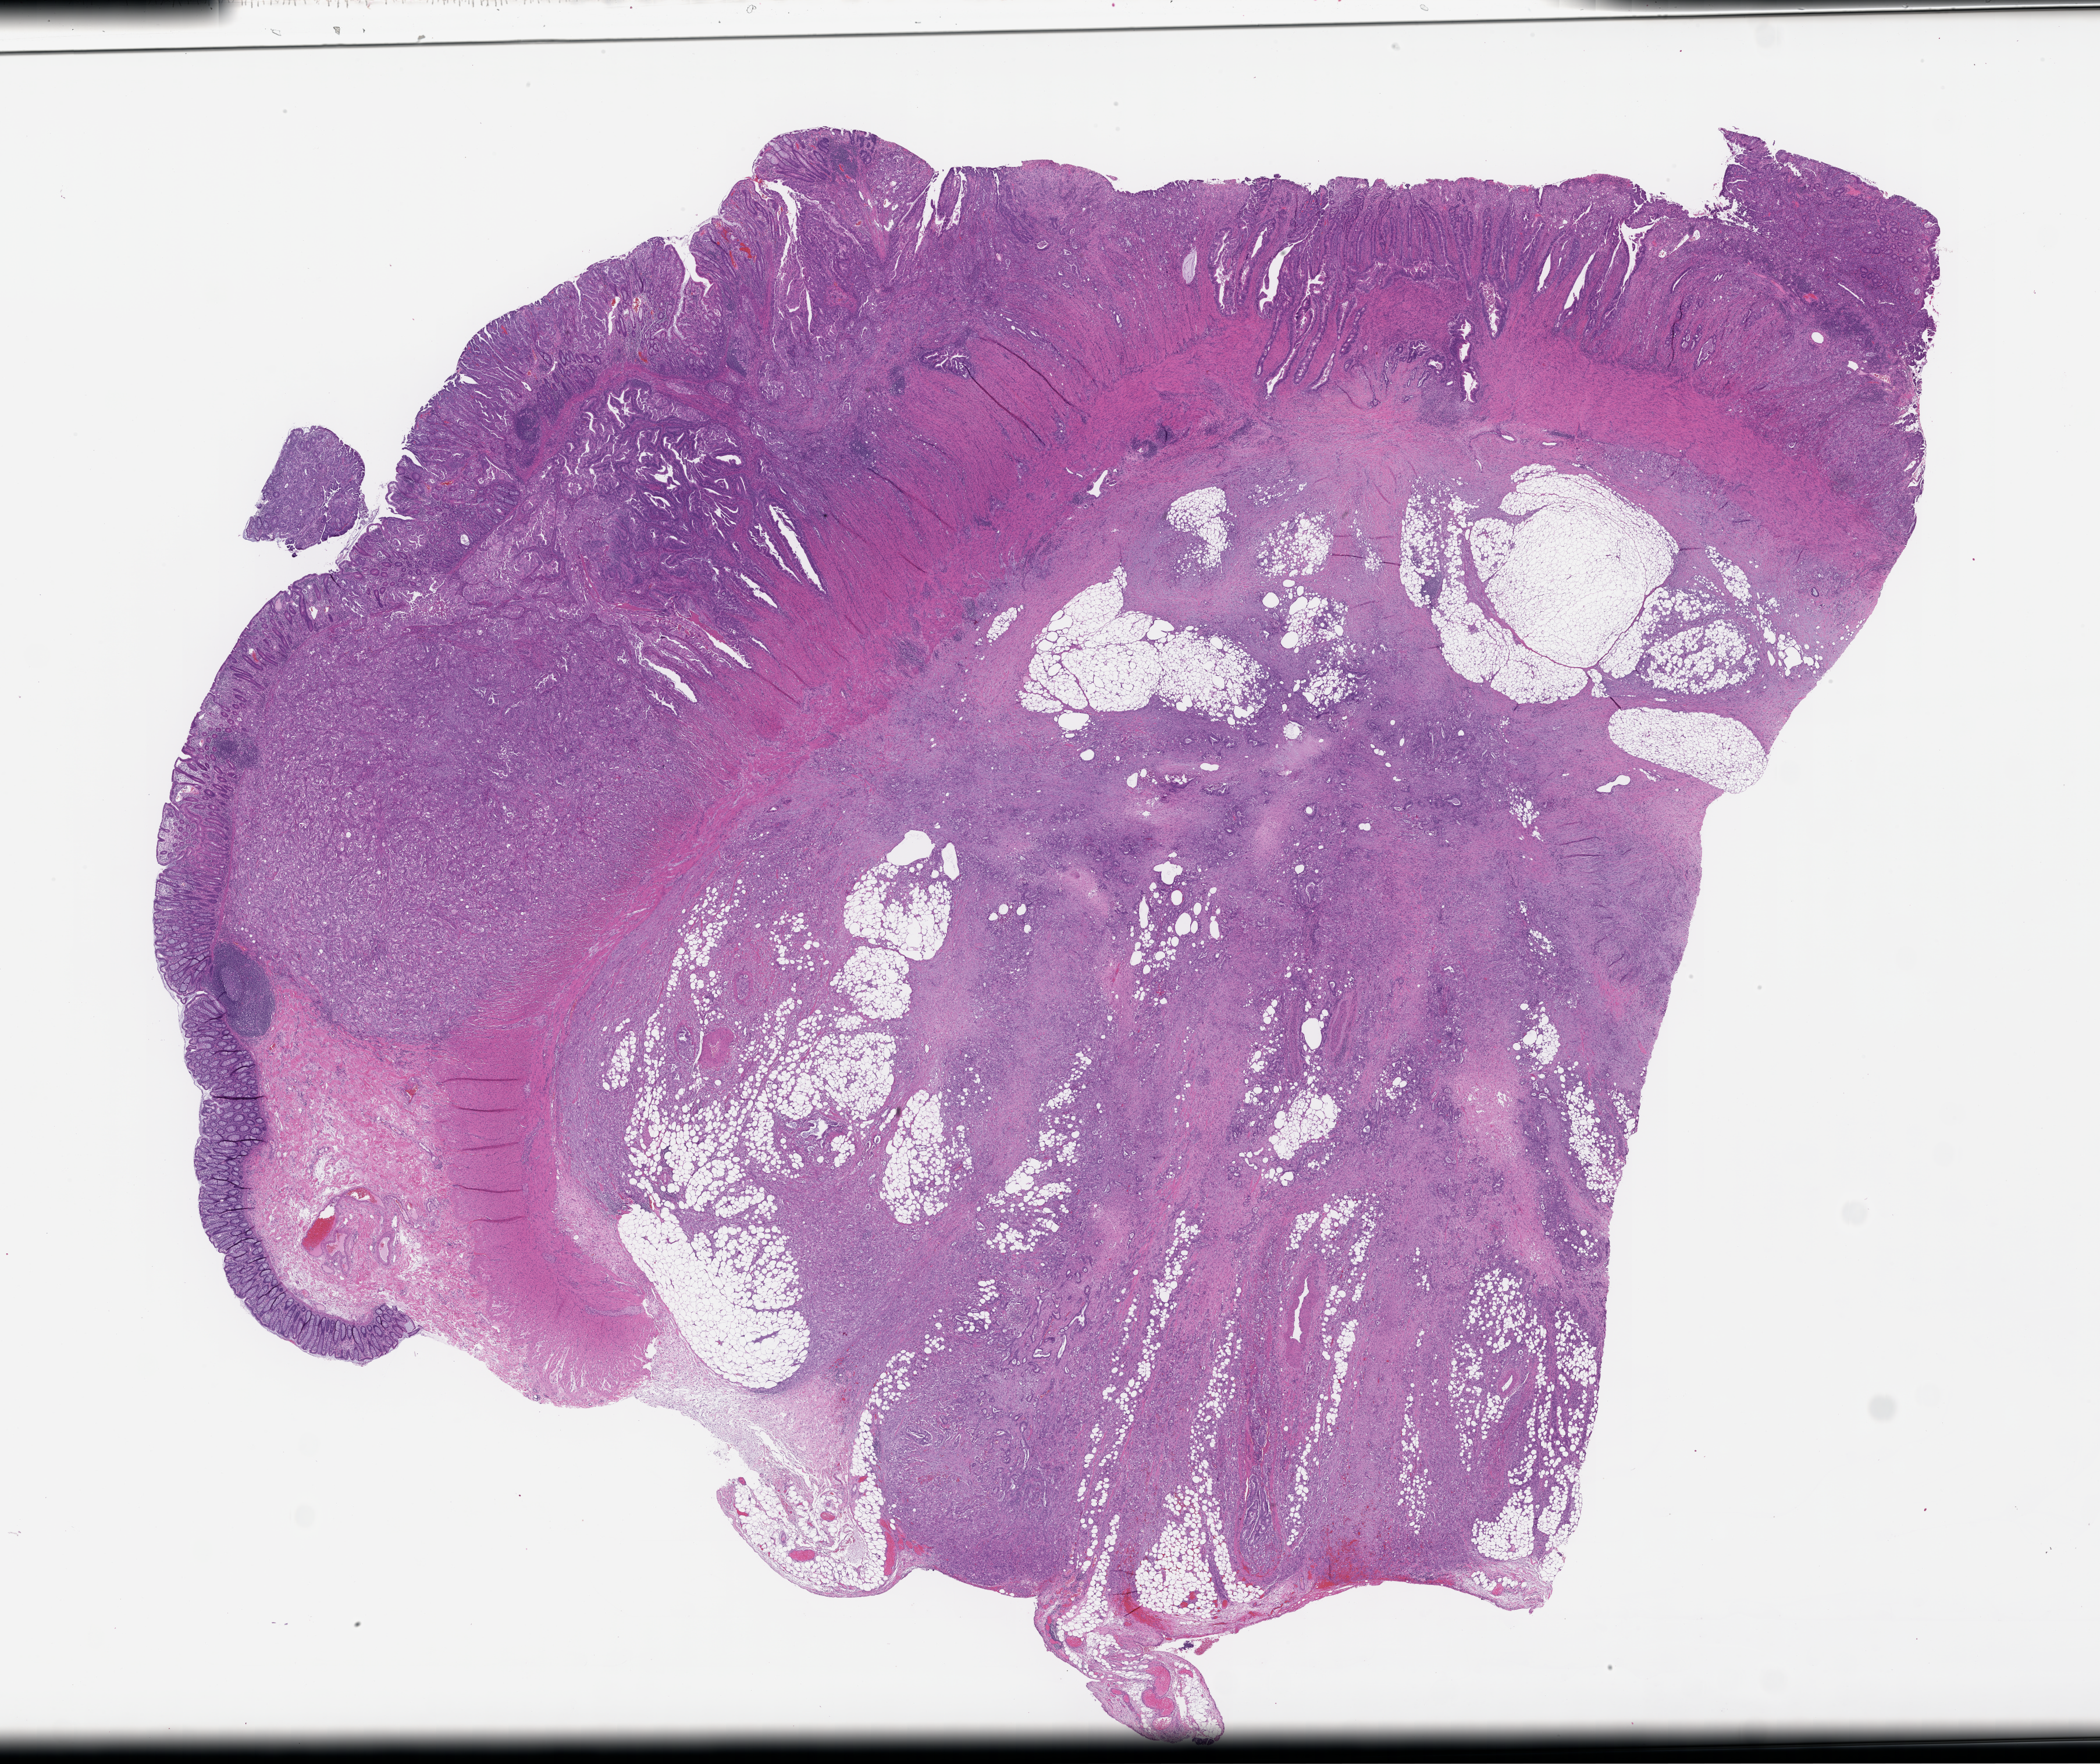
Digitized H&E-stained section — low-resolution overview of the scanned area, about 29.1 x 24.5 mm, FFPE section, site: colon, archival tissue. Patient sex: male.
This section: primary tumor. Diagnosis: Colorectal Carcinoma.